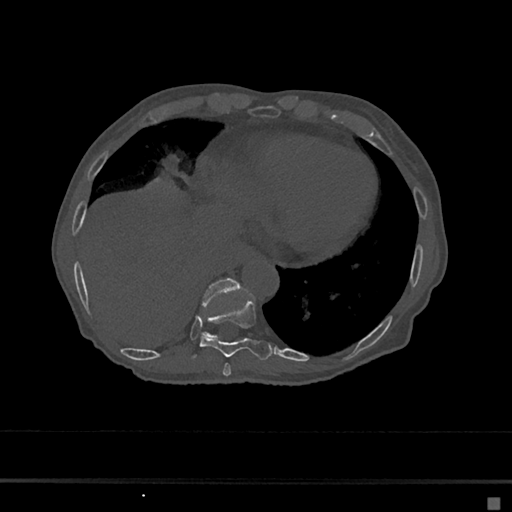
CT including the spine, one axial slice; 120 kVp; bone window (W 1800 / L 400 HU); 0.5 mm slice thickness; 512 × 512 image matrix. Female patient, age 68 years. From the clinical record (not read from this slice): primary cancer: renal.
Structures marked on this image (semi-automatic segmentation, software-assisted and operator-edited):
- T10 vertebra: box from (x=202, y=278) to (x=242, y=339) px
- T8 vertebra: (x=223, y=363)–(x=231, y=376)
- T9 vertebra: (x=192, y=299)–(x=274, y=361)